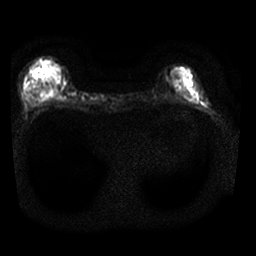
Breast MRI, one axial slice; slice 7 of 25 in the series (ordered by position); diffusion-weighted series; image 2 of 4 stored at this slice position (different b-values; order by instance number); 1.5 T; 4 mm slice thickness; 256 × 256 image matrix, field of view 310 × 310 mm. Female patient.
Annotated regions visible in this slice (manually delineated by an expert):
- tumour on diffusion-weighted imaging: bounding box [x1, y1, x2, y2] px = [55, 75, 60, 81]